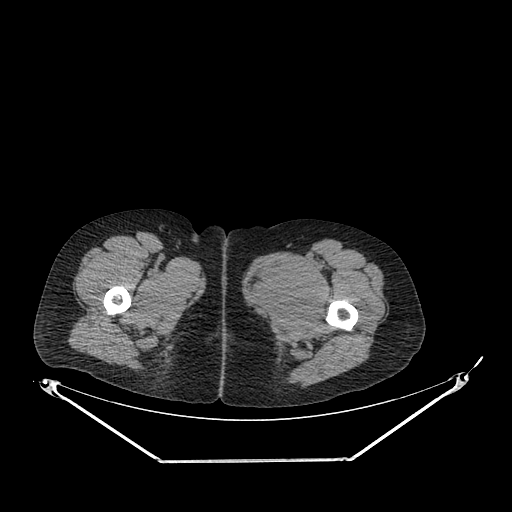
CT of an extremity soft-tissue mass (from a PET/CT study), one axial slice; slice 252 of 267 in the series (ordered by position); 120 kVp; soft-tissue window (W 400 / L 40 HU); 512 × 512 image matrix. Female patient. Case-level facts recorded for this patient, not image findings: histological type: pleiomorphic leiomyosarcoma; grade: intermediate; site of the primary tumour: left thigh.
Annotated regions visible in this slice (expert contour drawn on MRI and transferred to this co-registered scan by the dataset authors):
- gross tumour volume including surrounding oedema: bounding box [x1, y1, x2, y2] px = [249, 254, 321, 314]
- gross tumour volume (mass): [249, 254, 321, 314]